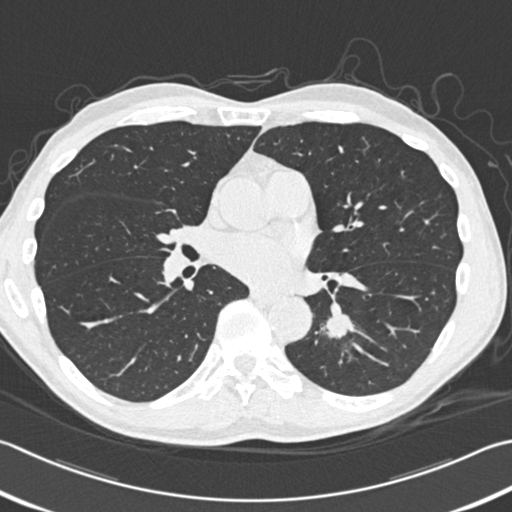
Low-dose screening chest CT, one axial slice; slice 177 of 354 in the series (ordered by position); 120 kVp; lung window (W 1500 / L -600 HU); 512 × 512 image matrix, field of view 346 × 346 mm.
Outlined on this slice (outlined manually by an expert reader):
- lesion 1 (tumor, lower lobe of left lung): bounding box <326,313,353,339> (left, top, right, bottom; pixels)